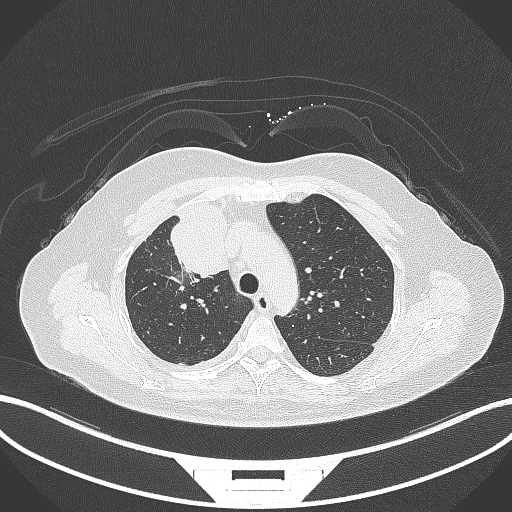
Chest CT, one axial slice; slice 220 of 305 in the series (ordered by position); reconstruction kernel B70f; 120 kVp; lung window (W 1500 / L -600 HU); 1 mm slice thickness; 512 × 512 image matrix, field of view 400 × 400 mm. Patient: female, 52 years. Case-level facts recorded for this patient, not image findings: clinical TNM (as recorded): T3 N1 M1.
Annotated regions visible in this slice (rectangle marked by the reading radiologist):
- lung tumour (recorded histology: adenocarcinoma): bounding box (x1, y1, x2, y2) in pixels: (165, 200, 231, 278)